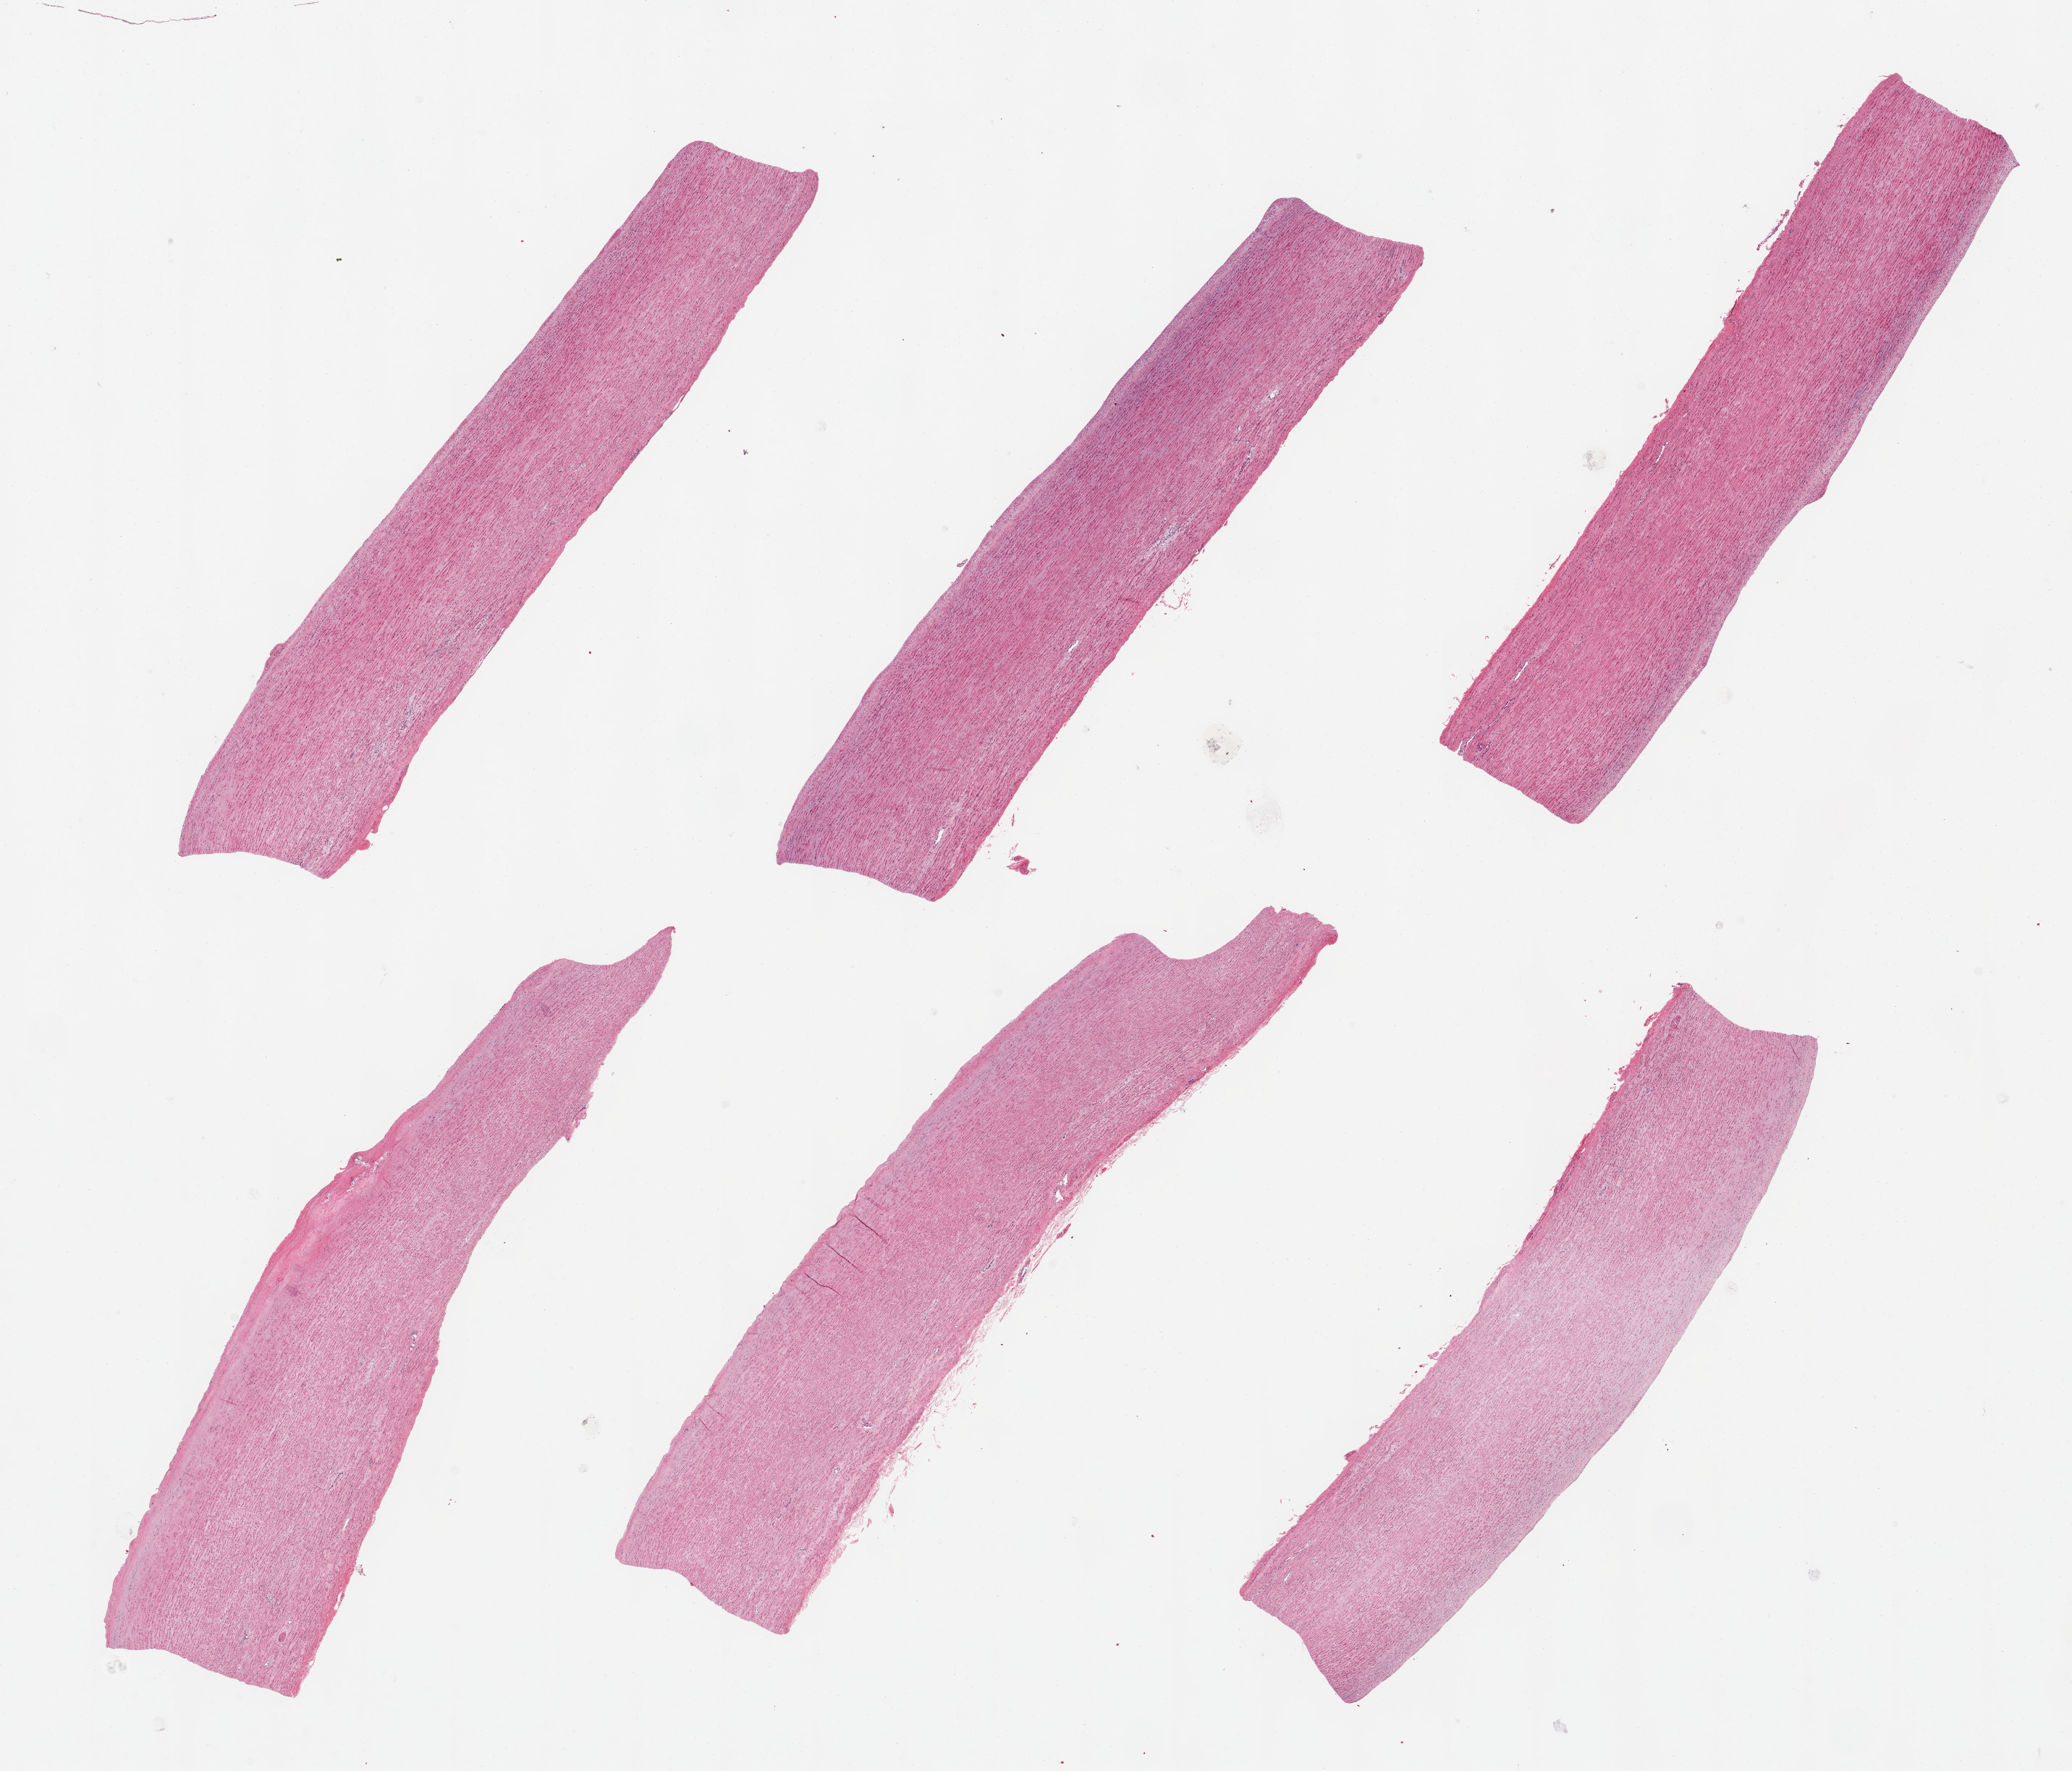
Digitized haematoxylin and eosin-stained section, low-resolution overview of the scanned area, about 22.6 x 19.4 mm; PAXgene-fixed paraffin-embedded (PFPE) section; sampled site (target tissue): aorta; tissue donor sample. Donor sex: male.
* pathologist's review note for this sample: 6 pieces, ~9x2mm. Several with layer of atherosis, up to 0.5mm in areas